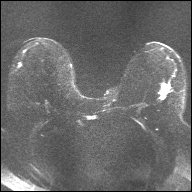
Breast MRI, one axial slice; position 15 of 32 along the scan axis; diffusion-weighted series; image 2 of 4 stored at this slice position (different b-values; order by instance number); 1.5 T; 4 mm slice thickness; 192 × 192 image matrix. Female patient.
Structures marked on this image (outlined manually by an expert reader):
- tumour on diffusion-weighted imaging: bounding box <160,85,170,99> (left, top, right, bottom; pixels)